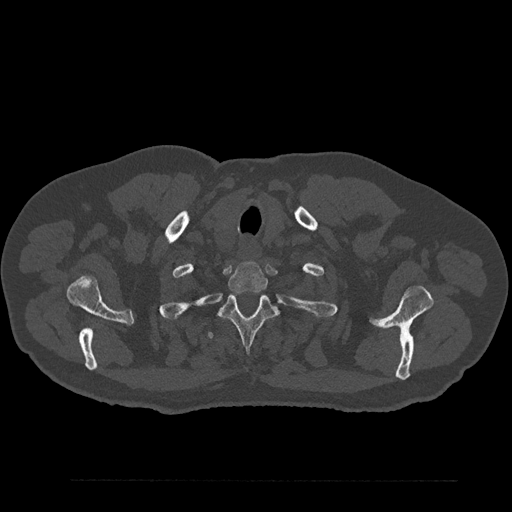
CT including the spine, one axial slice; slice 724 of 797 in the series (ordered by position); reconstruction kernel Br40s/3; bone window (W 1800 / L 400 HU); 0.5 mm slice thickness; 512 × 512 image matrix. Patient: male, 61 years. From the clinical record (not read from this slice): primary cancer: prostate.
Outlined on this slice (semi-automatic segmentation, software-assisted and operator-edited):
- T1 vertebra: bounding box (x1, y1, x2, y2) in pixels: (228, 262, 268, 293)
- T2 vertebra: (220, 294, 278, 352)
- T3 vertebra: (205, 331, 214, 340)